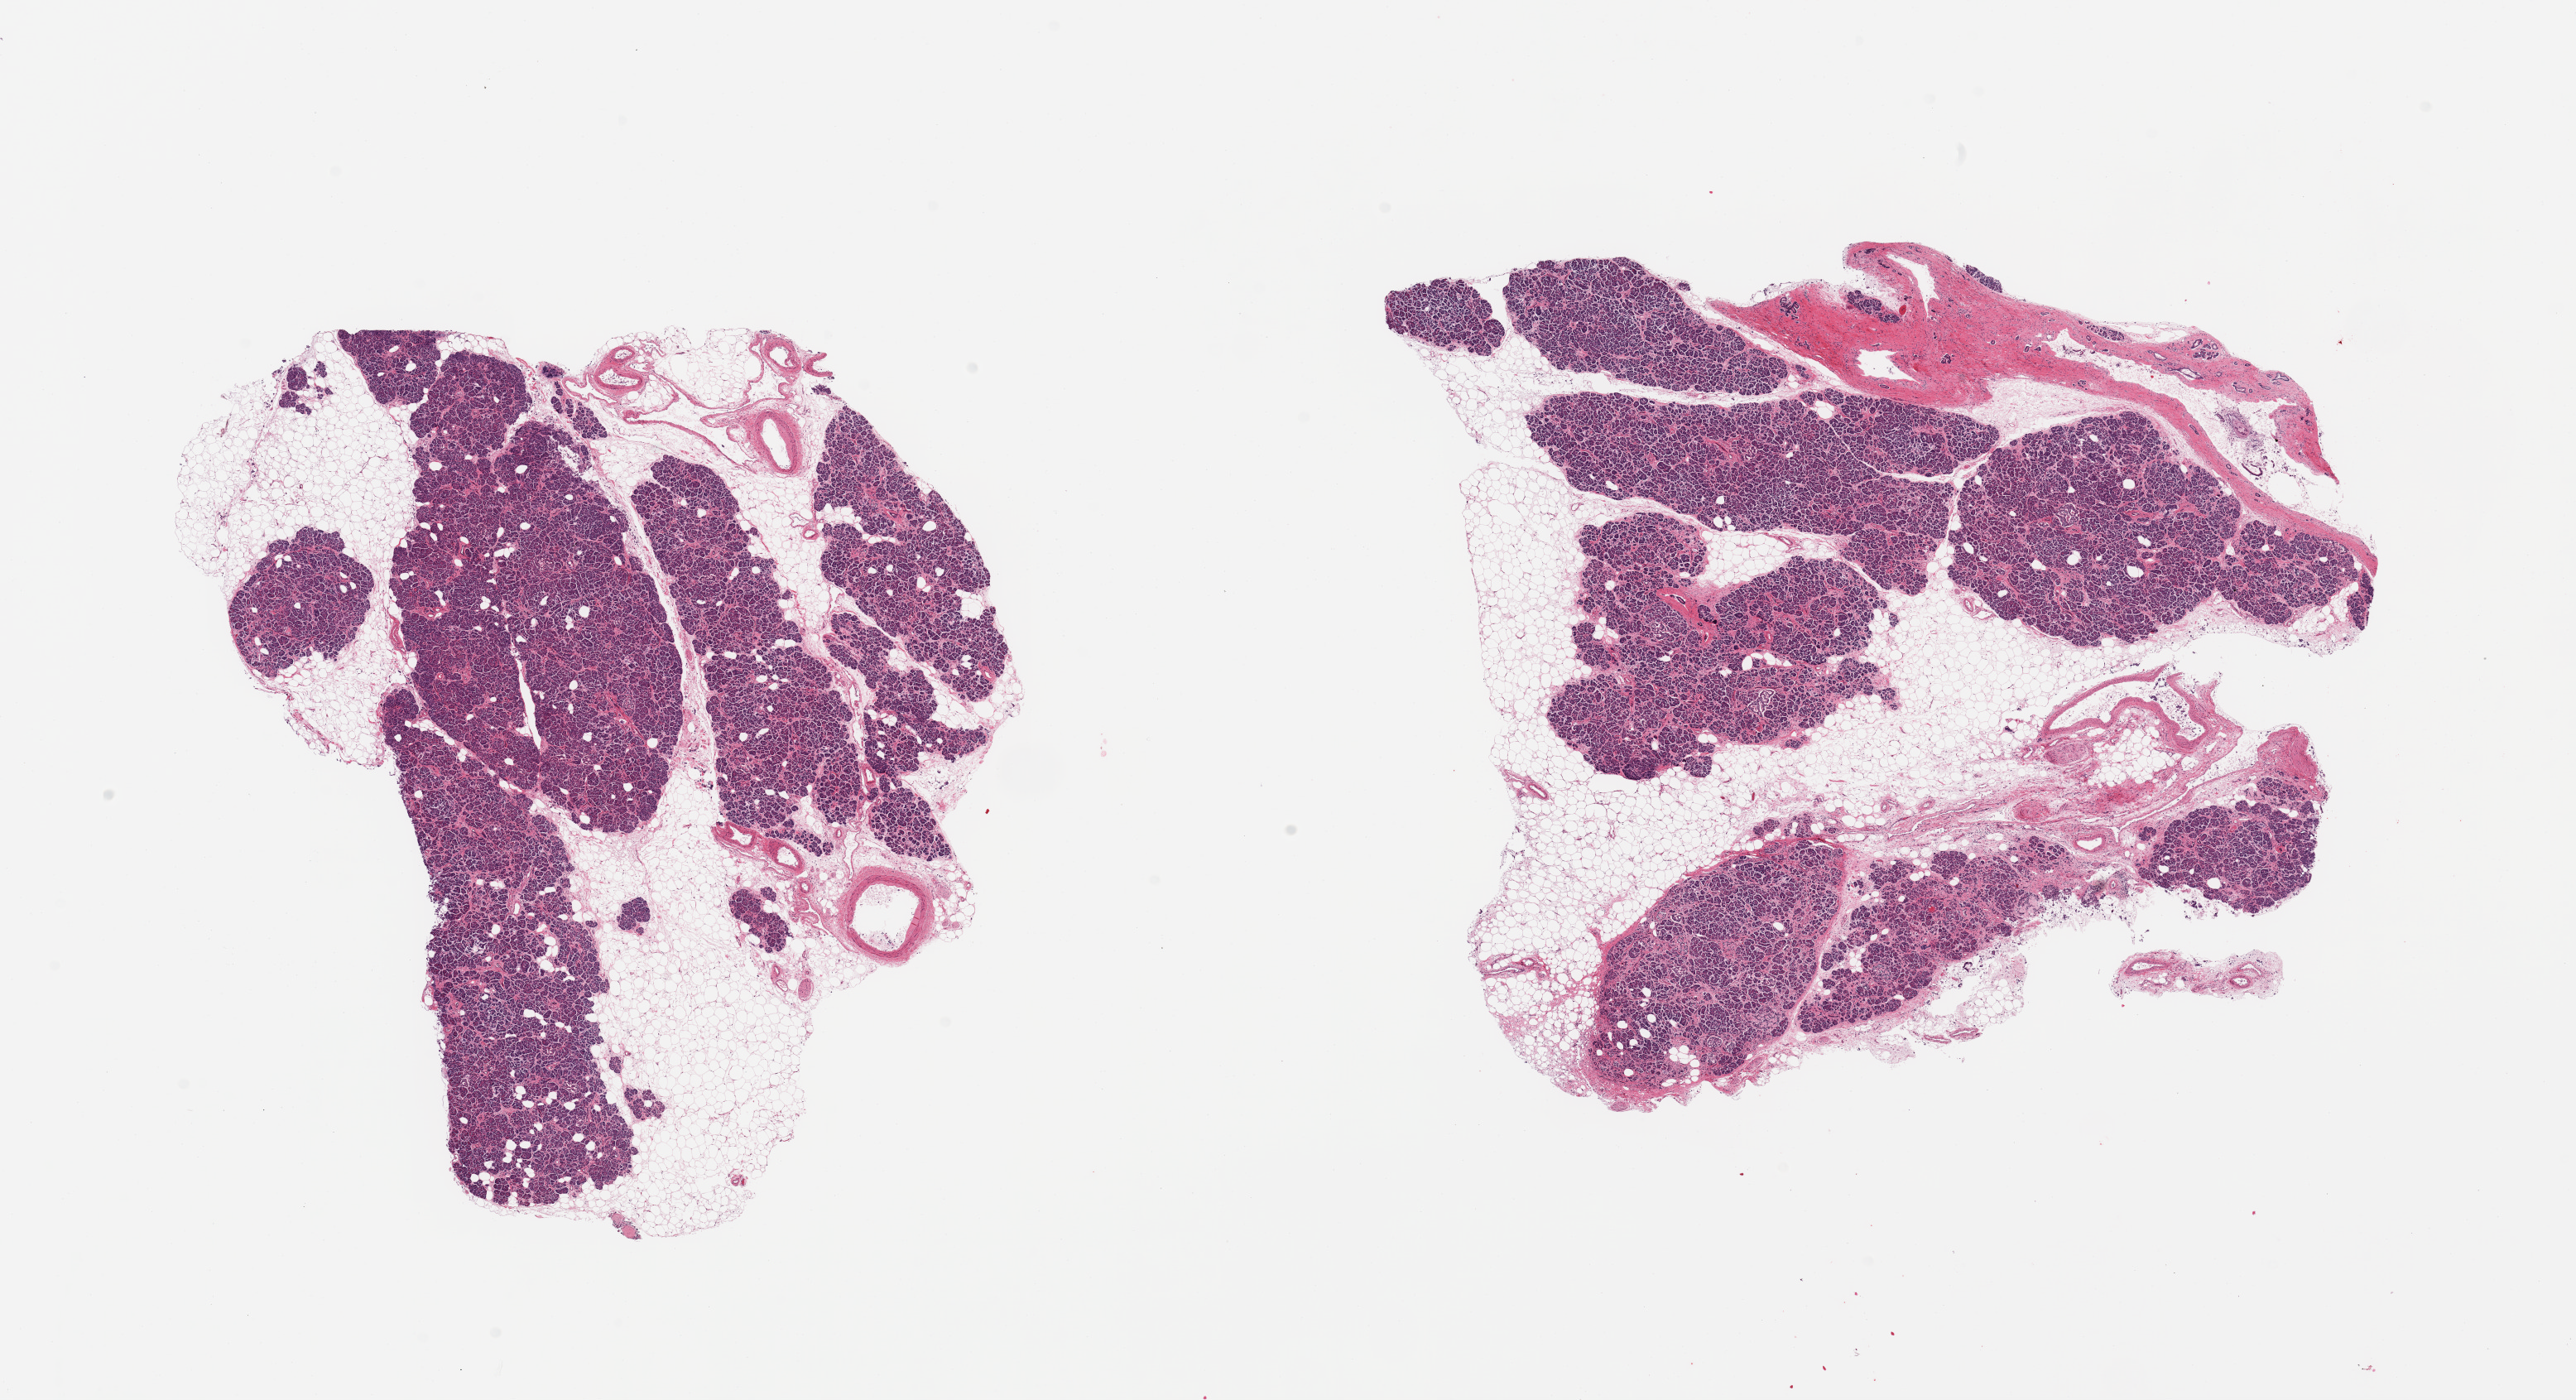
H&E whole-slide image, brightfield, low-resolution overview of the scanned area, about 24.6 x 13.4 mm (slide scanned at 20x). PAXgene-fixed paraffin-embedded (PFPE) section. Section of pancreas (target tissue). Tissue donor sample. Female donor.
Pathologist's review note for this sample: 2 pieces; 30% & 40% internal fat; areas of interstitial fibrosis.